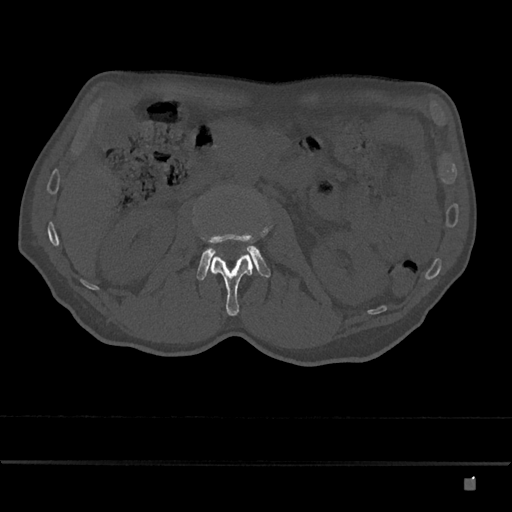
CT including the spine, one axial slice. Slice 451 of 797 in the series (ordered by position). 120 kVp. Bone window (W 1800 / L 400 HU). 512 × 512 image matrix, field of view 390 × 390 mm. Patient: male, 72 years. From the clinical record (not read from this slice): primary cancer: prostate.
Outlined on this slice (semi-automatic segmentation, software-assisted and operator-edited):
- L2 vertebra: bounding box [x1, y1, x2, y2] px = [208, 226, 269, 316]
- L3 vertebra: [197, 246, 271, 280]